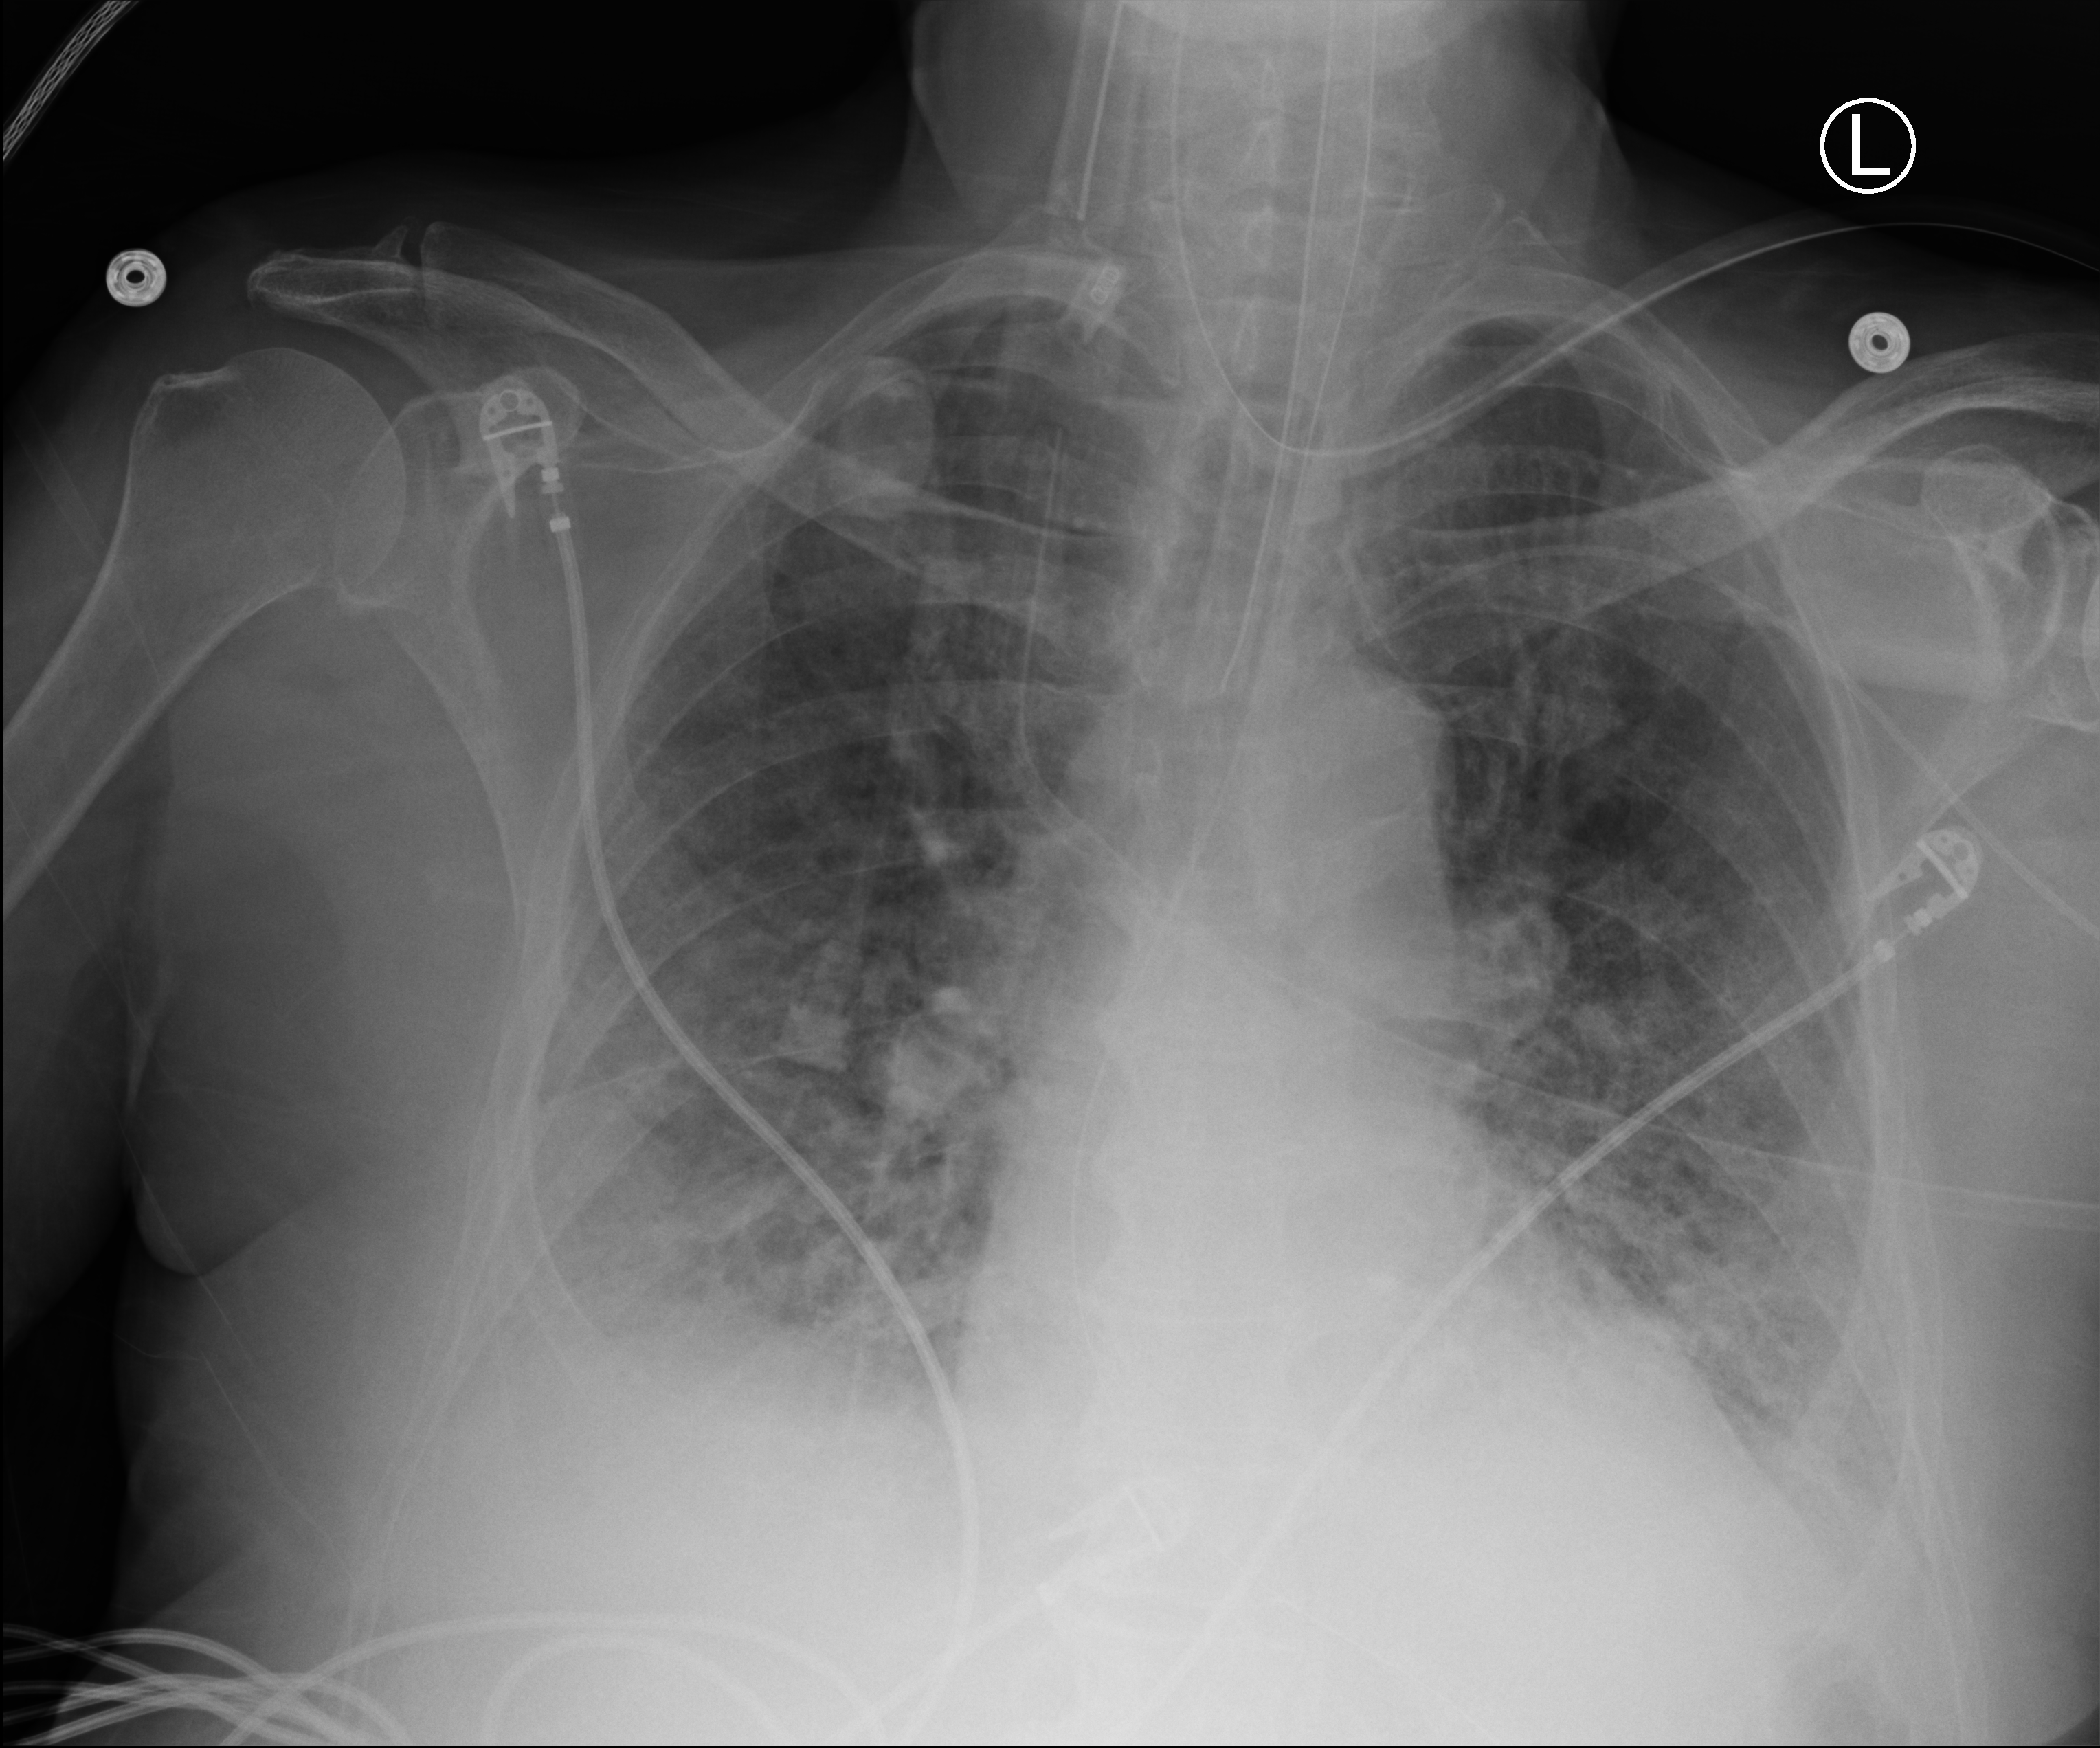
Bedside chest radiograph (computed radiography); anteroposterior (AP) projection. Patient hospitalised with COVID-19; male, aged 75–90 years.
Admission-level facts for this patient (not findings on this image; timing relative to this image not recorded):
- hypertension (admission record): no
- mechanically ventilated during this hospital stay: yes